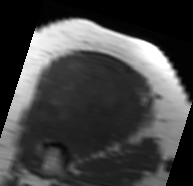
MRI of an extremity soft-tissue mass, one axial slice. Position 48 of 91 along the scan axis. MR volume resampled by the dataset authors to the PET/CT grid (not the native acquisition matrix). 3.27 mm slice thickness. 193 × 186 image matrix, field of view 188 × 182 mm. Female patient. From the clinical record (not read from this slice): histological type: malignant solitary fibrous tumor; grade: intermediate; site of the primary tumour: right thigh.
Structures marked on this image (expert contour drawn on MRI and transferred to this co-registered scan by the dataset authors):
- gross tumour volume including surrounding oedema: bounding box <19,55,148,152> (left, top, right, bottom; pixels)
- gross tumour volume (mass): <24,55,146,150>